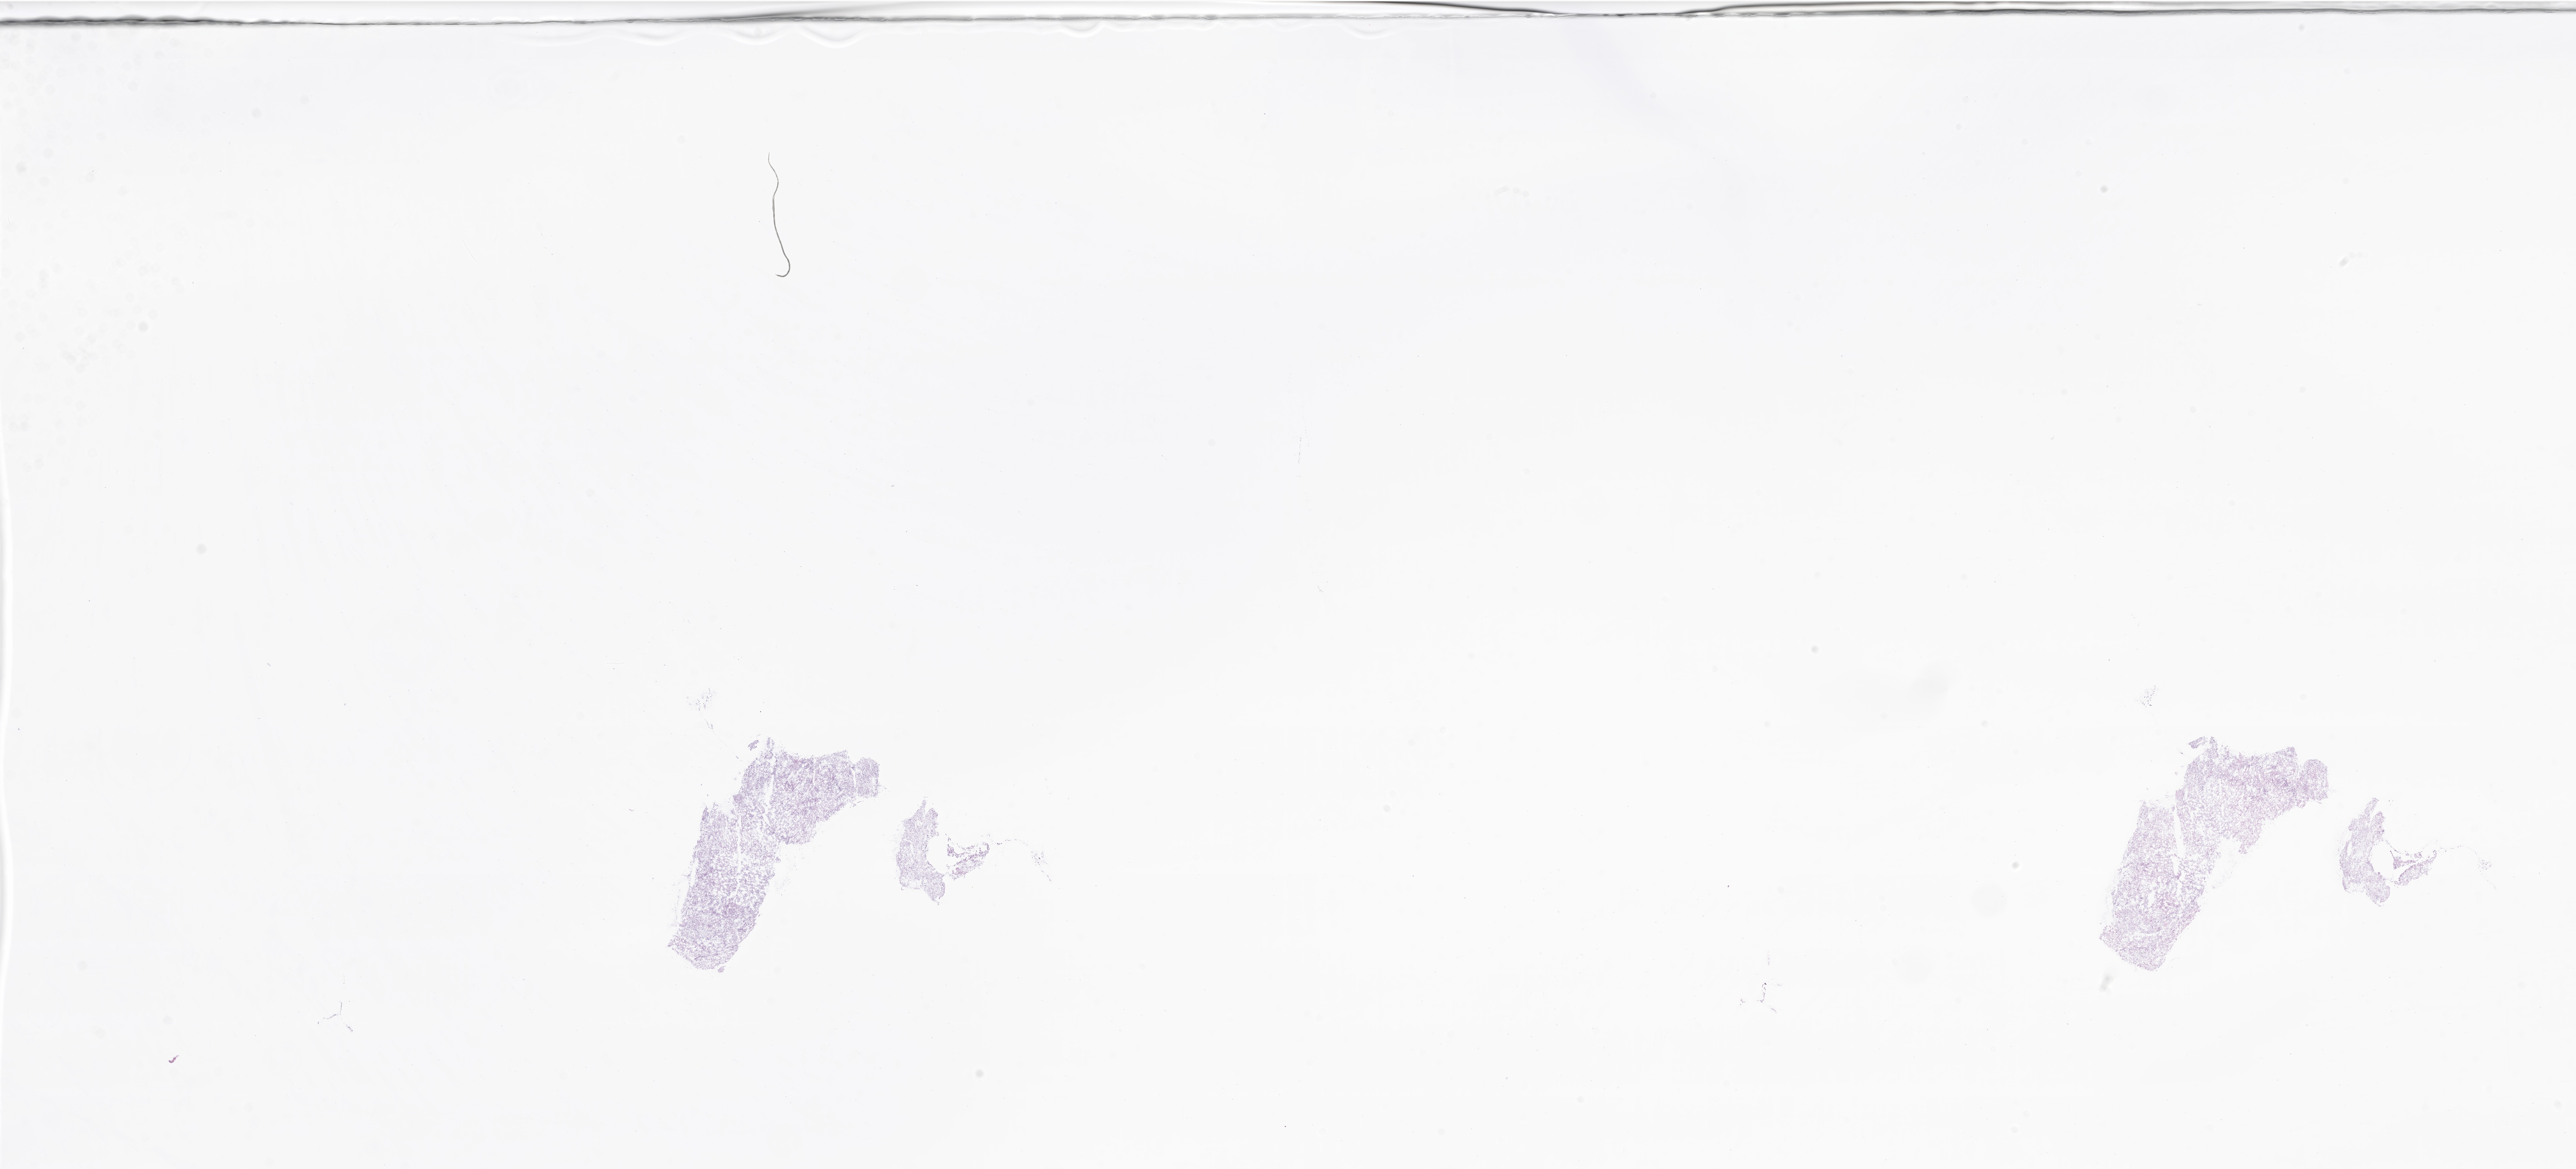
Digitized hematoxylin and eosin (H&E)-stained section of tumor tissue from the brain, low-resolution overview of the scanned area, about 37.1 x 16.8 mm; frozen section (OCT-embedded). Male patient, age 481 days (about 1.3 years).
Recorded diagnosis: Neoplasm, malignant.